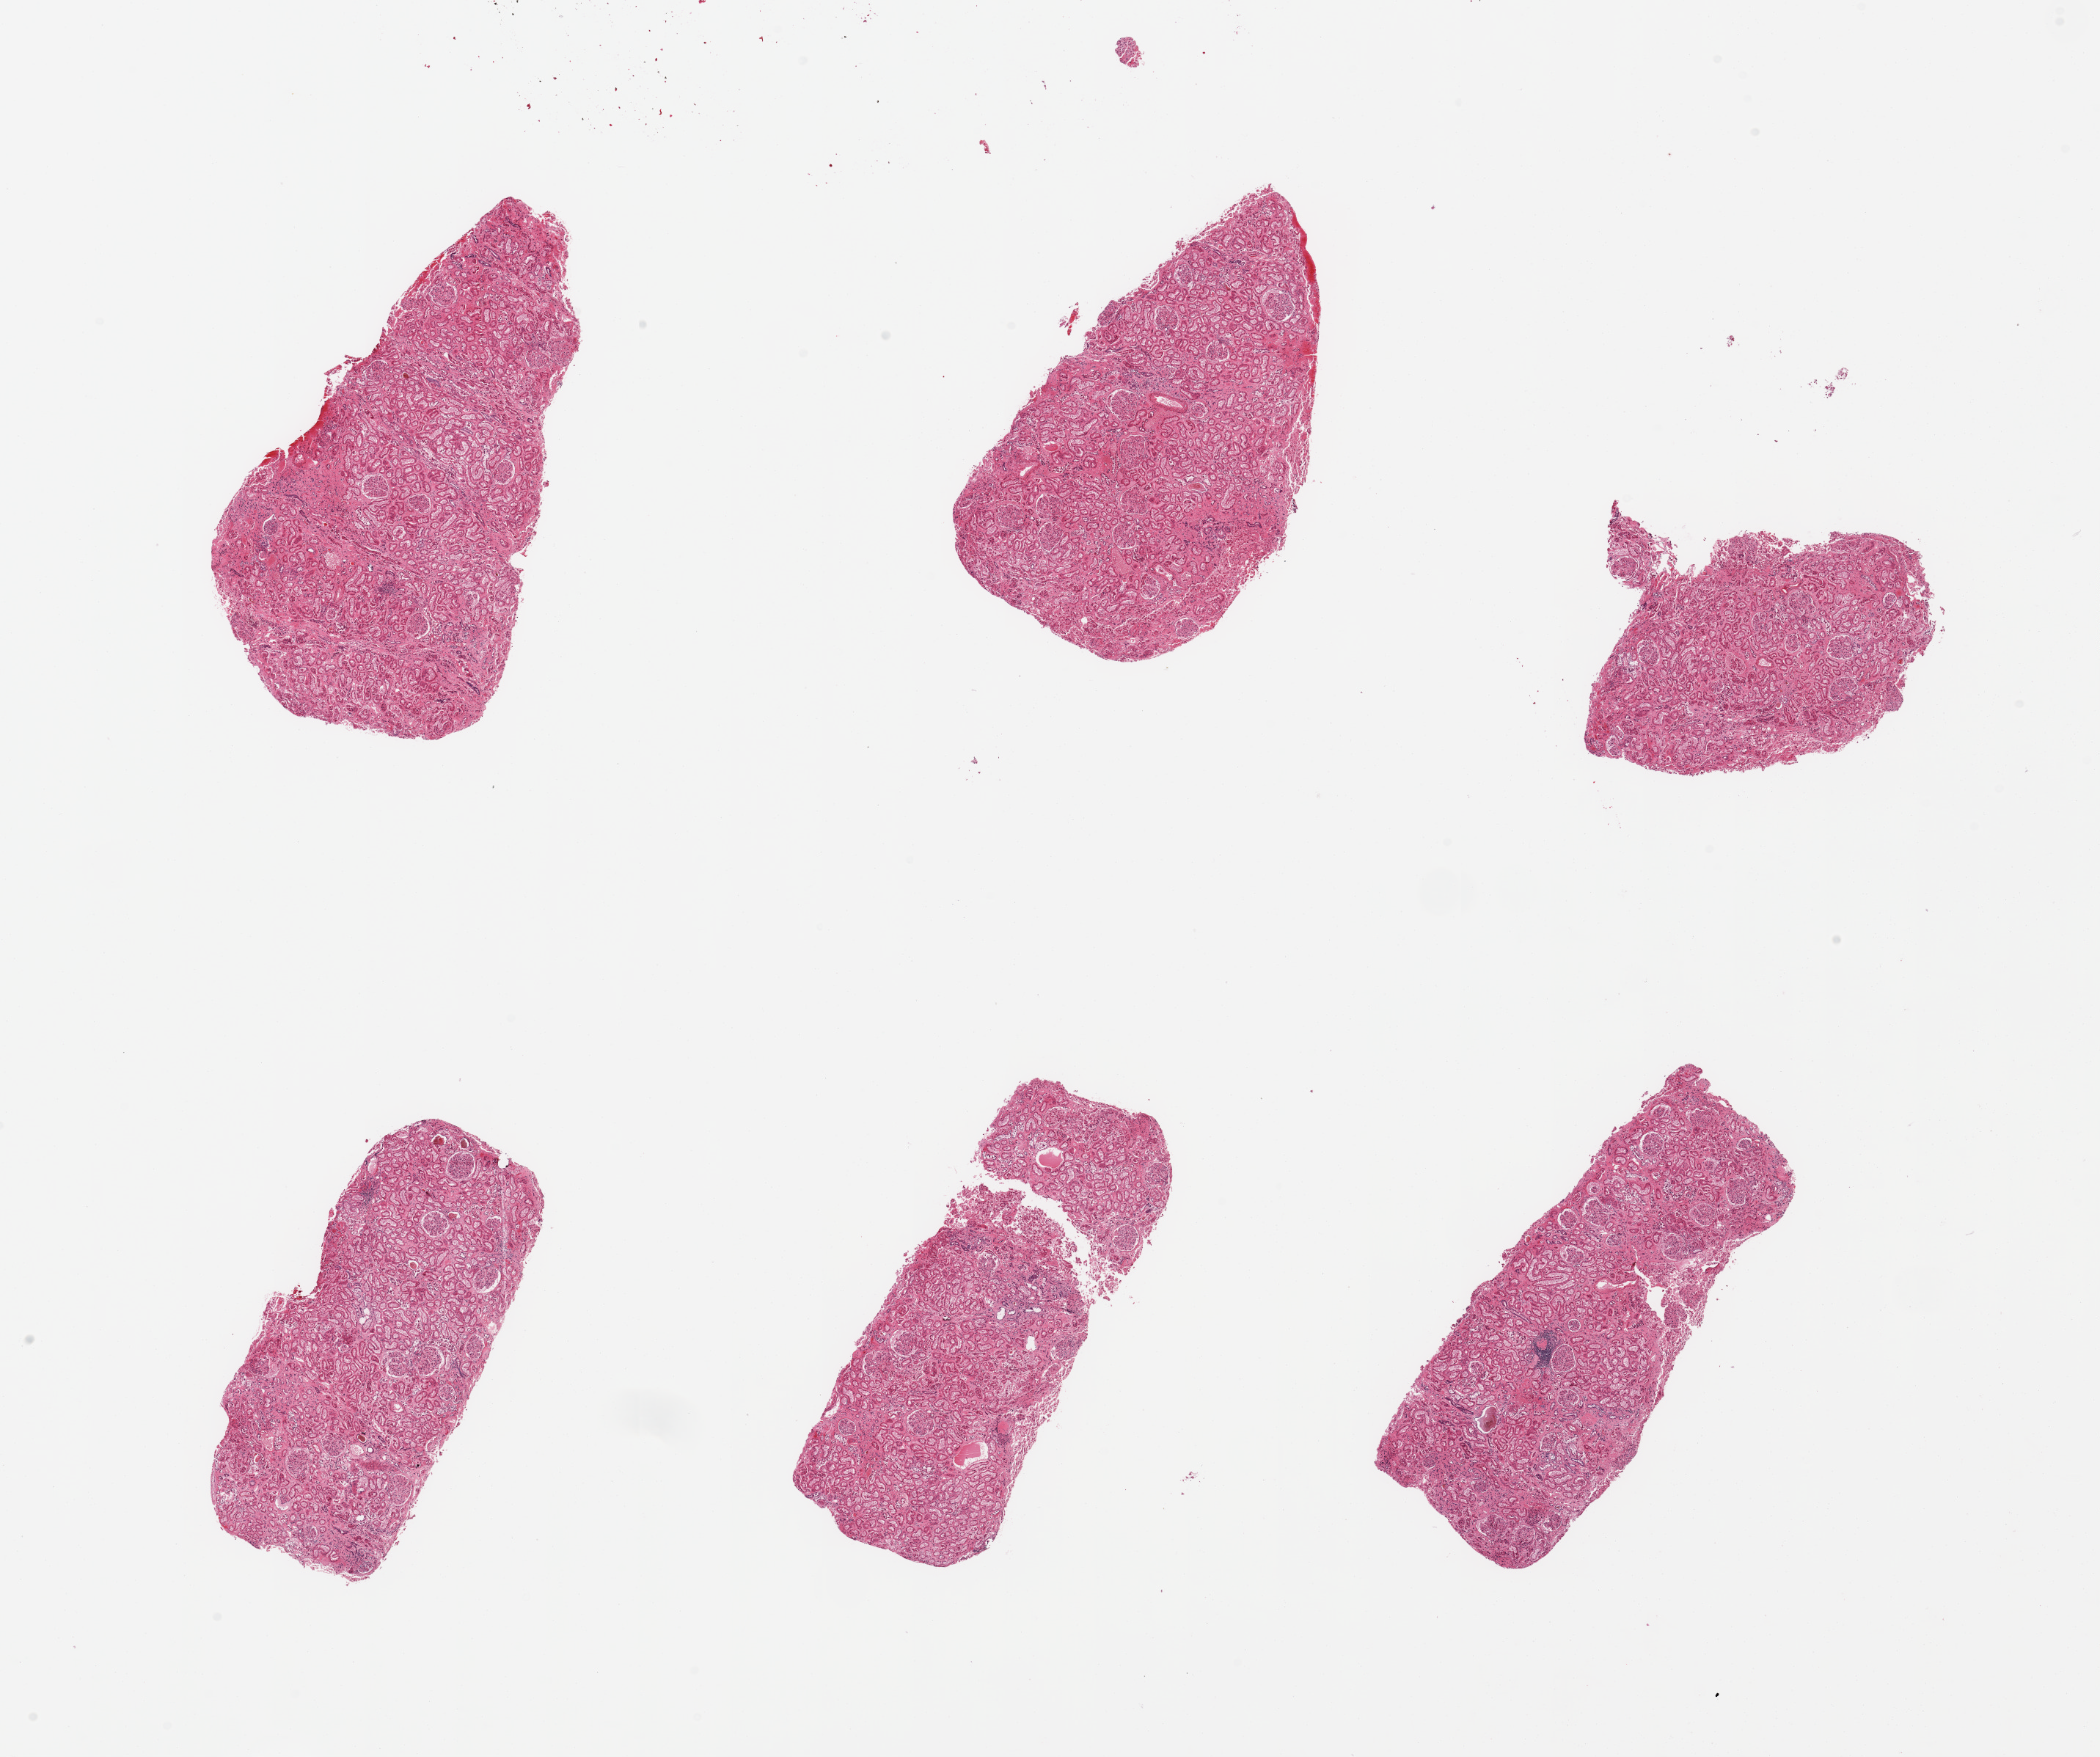
Whole-slide image, haematoxylin and eosin stain, brightfield — a low-resolution overview of the entire scanned area, about 22.6 x 18.9 mm (acquisition: 20x scan). PAXgene-fixed paraffin-embedded (PFPE) section. Sampled site (target tissue): renal cortex. Donor tissue sample. Donor: male.
Reviewer comment on this tissue sample: 6 pieces, glomerulie present, tubules with moderately advanced autolysis.